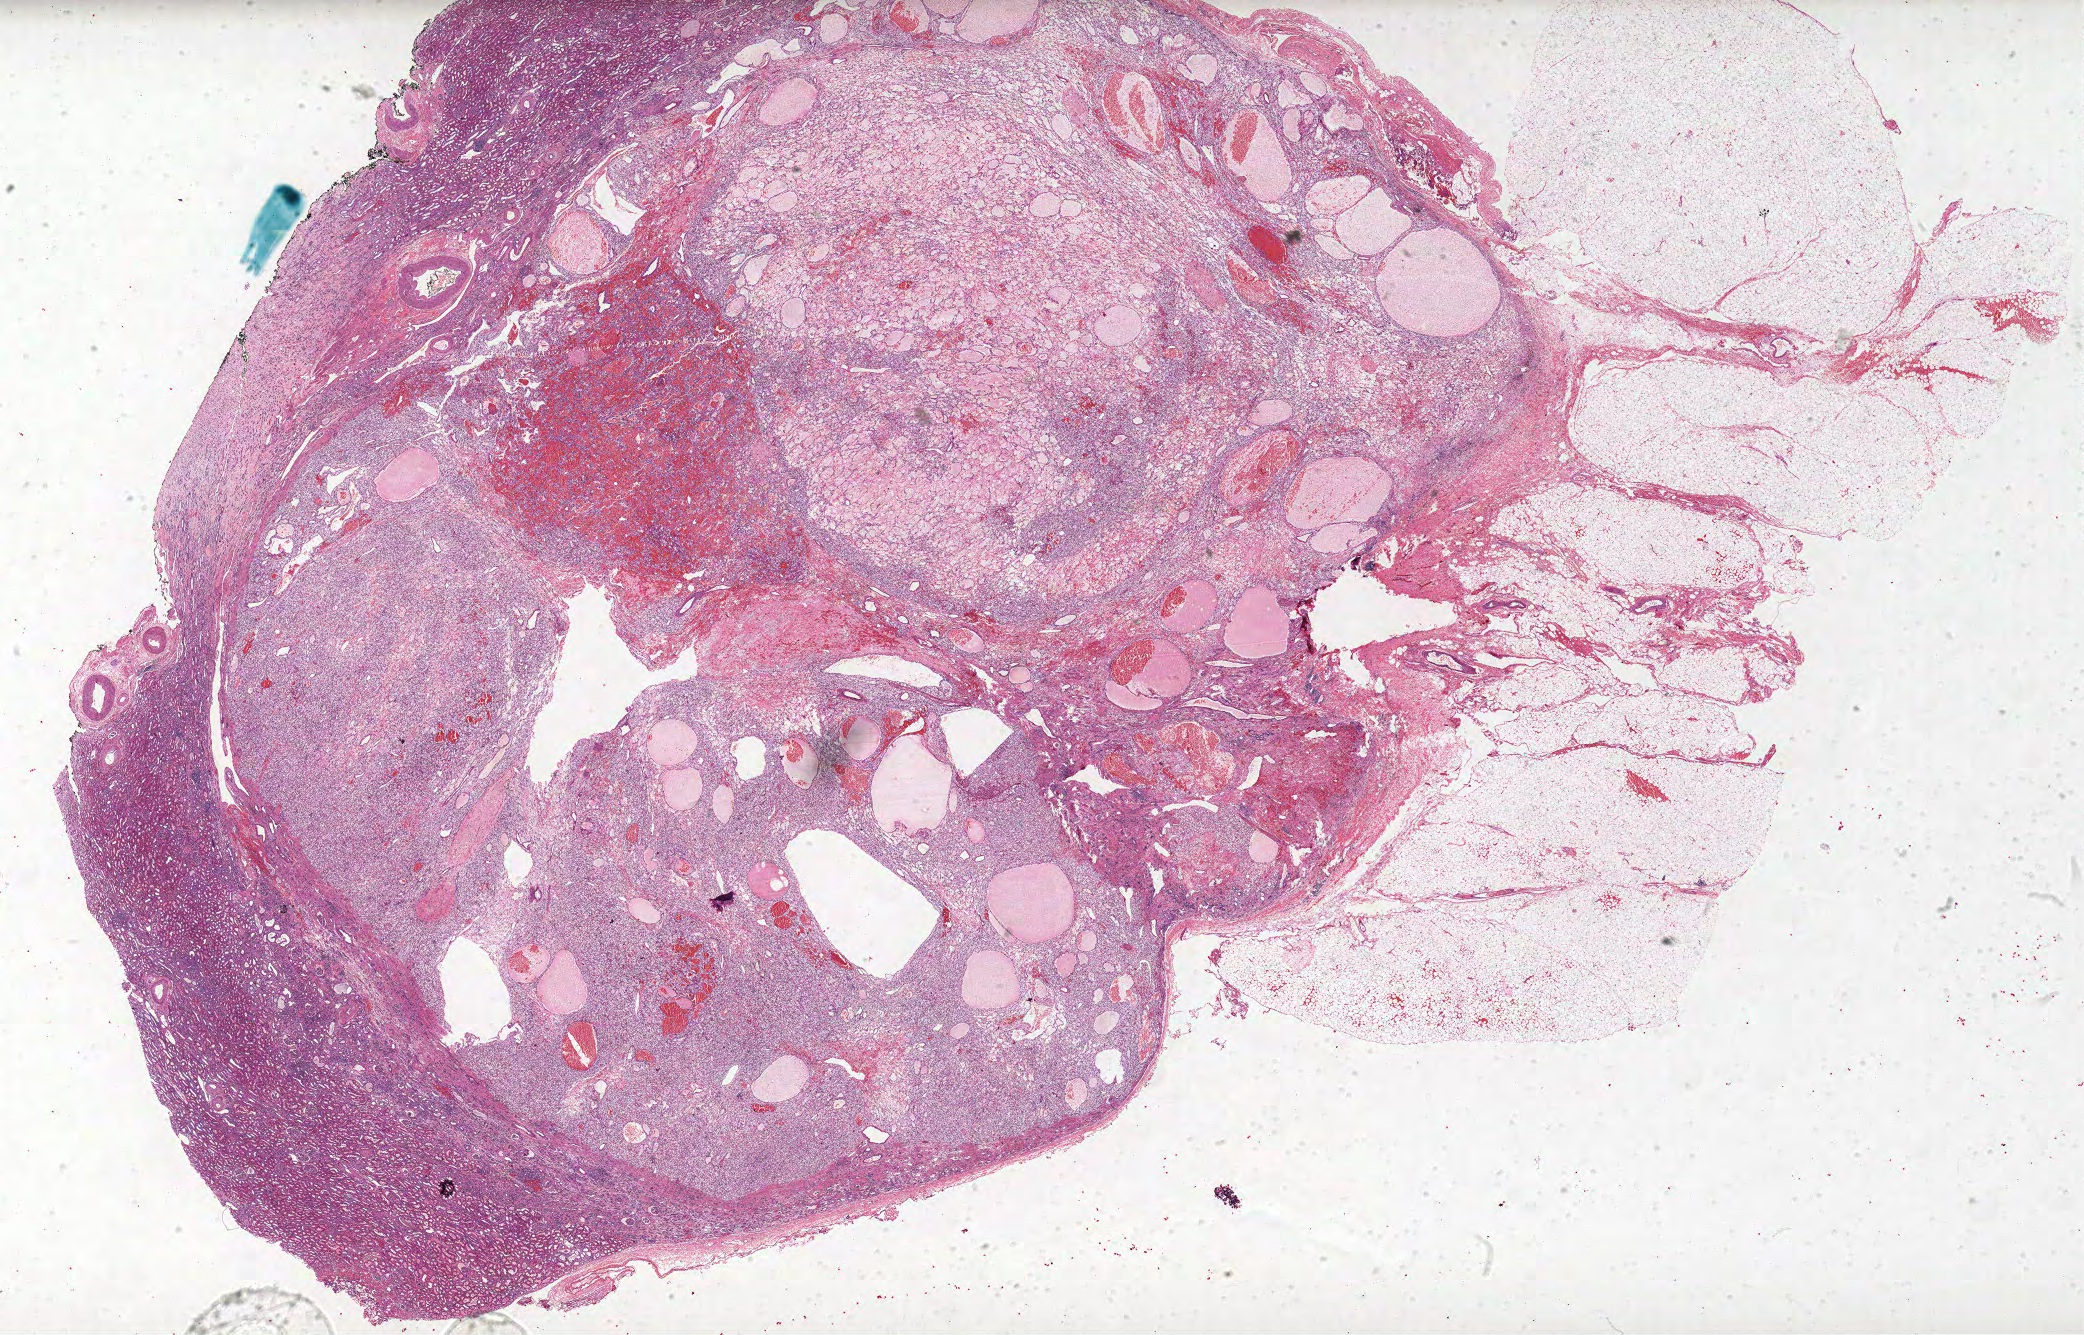
H&E whole-slide image — a low-resolution overview of the entire scanned area, about 33.3 x 21.3 mm (from a 40x scan). FFPE section. Primary tumour sample from the kidney. Female, age 75 years at initial diagnosis. Histologic grade: G2 (moderately differentiated).
AJCC pathologic stage: I. TNM: T1a NX M0. Histologic diagnosis: Clear cell adenocarcinoma, NOS.